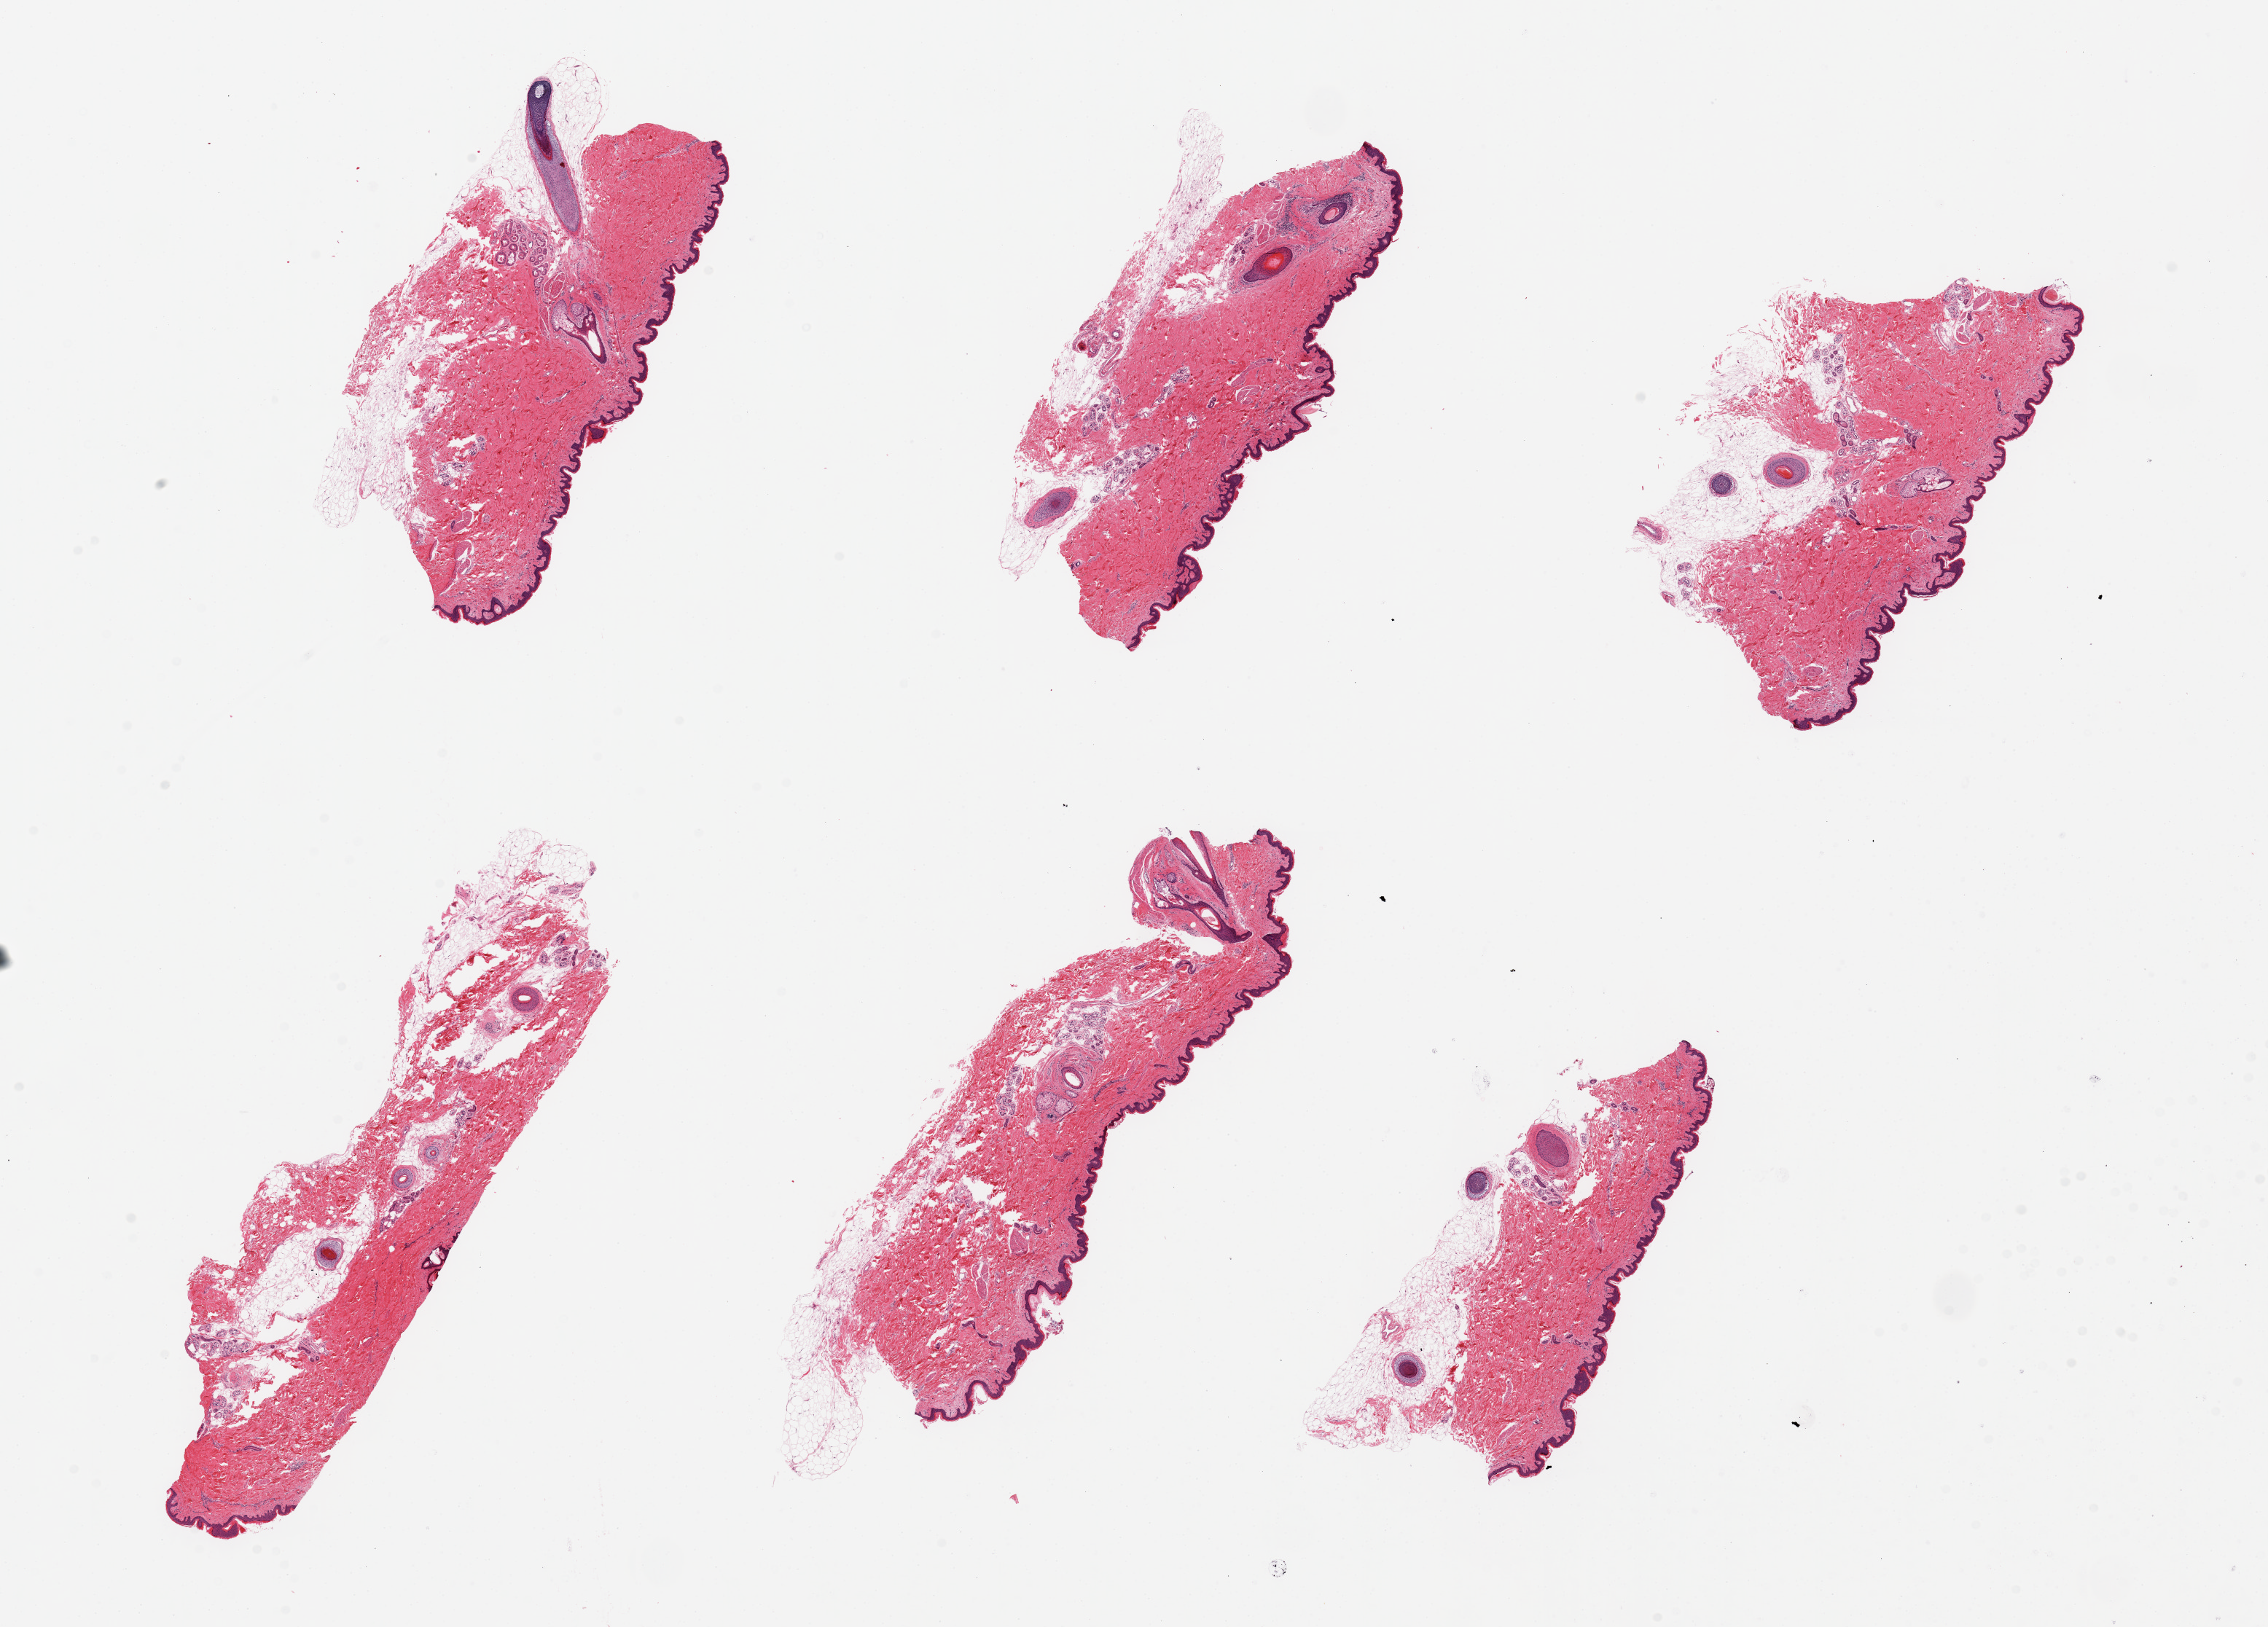
Digitized haematoxylin and eosin-stained section, brightfield — whole scanned area (about 24.6 x 17.7 mm, from a 20x scan) shown as a low-resolution overview, PAXgene-fixed, paraffin-embedded tissue, sampled site (target tissue): skin of suprapubic region, donor tissue sample. Donor sex: male.
* reviewer comment on this tissue sample: 6 pieces, up to 8.5x2mm; squamous epithelium is ~1% thickness